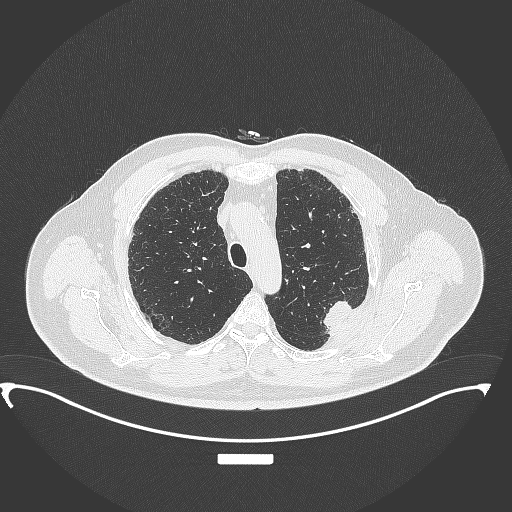
Chest CT, one axial slice. Slice 276 of 350 in the series (ordered by position). Lung window (W 1500 / L -600 HU). 1 mm slice thickness. 512 × 512 image matrix. Male patient, age 64 years. Case-level facts recorded for this patient, not image findings: clinical TNM (as recorded): T1c N1 M1.
Structures marked on this image (rectangle marked by the reading radiologist):
- lung tumour (recorded histology: adenocarcinoma): bounding box <316,294,362,336> (left, top, right, bottom; pixels)